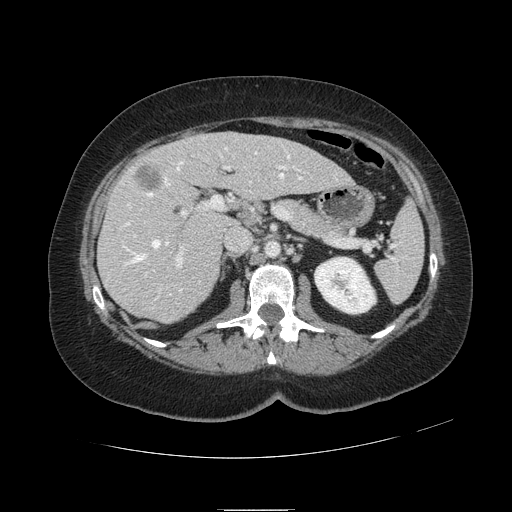
Contrast-enhanced abdominal CT, one axial slice. Slice 58 of 121 in the series (ordered by position). Soft-tissue window (W 400 / L 40 HU). 2.5 mm slice thickness. 512 × 512 image matrix, field of view 400 × 400 mm. Female patient, age 52 years. From the clinical record (not read from this slice): diagnosis: colorectal cancer liver metastases, imaged before liver resection; multiple liver metastases: yes; largest metastasis: 6.3 cm; chemotherapy before resection: yes.
Outlined on this slice (expert manual segmentation):
- hepatic veins: bounding box [x1, y1, x2, y2] px = [124, 148, 302, 295]
- liver: [99, 133, 351, 323]
- planned liver remnant (the part of the liver to remain after resection): [168, 133, 350, 200]
- portal vein (with intrahepatic branches): [126, 166, 299, 267]
- liver metastasis: [136, 167, 160, 189]